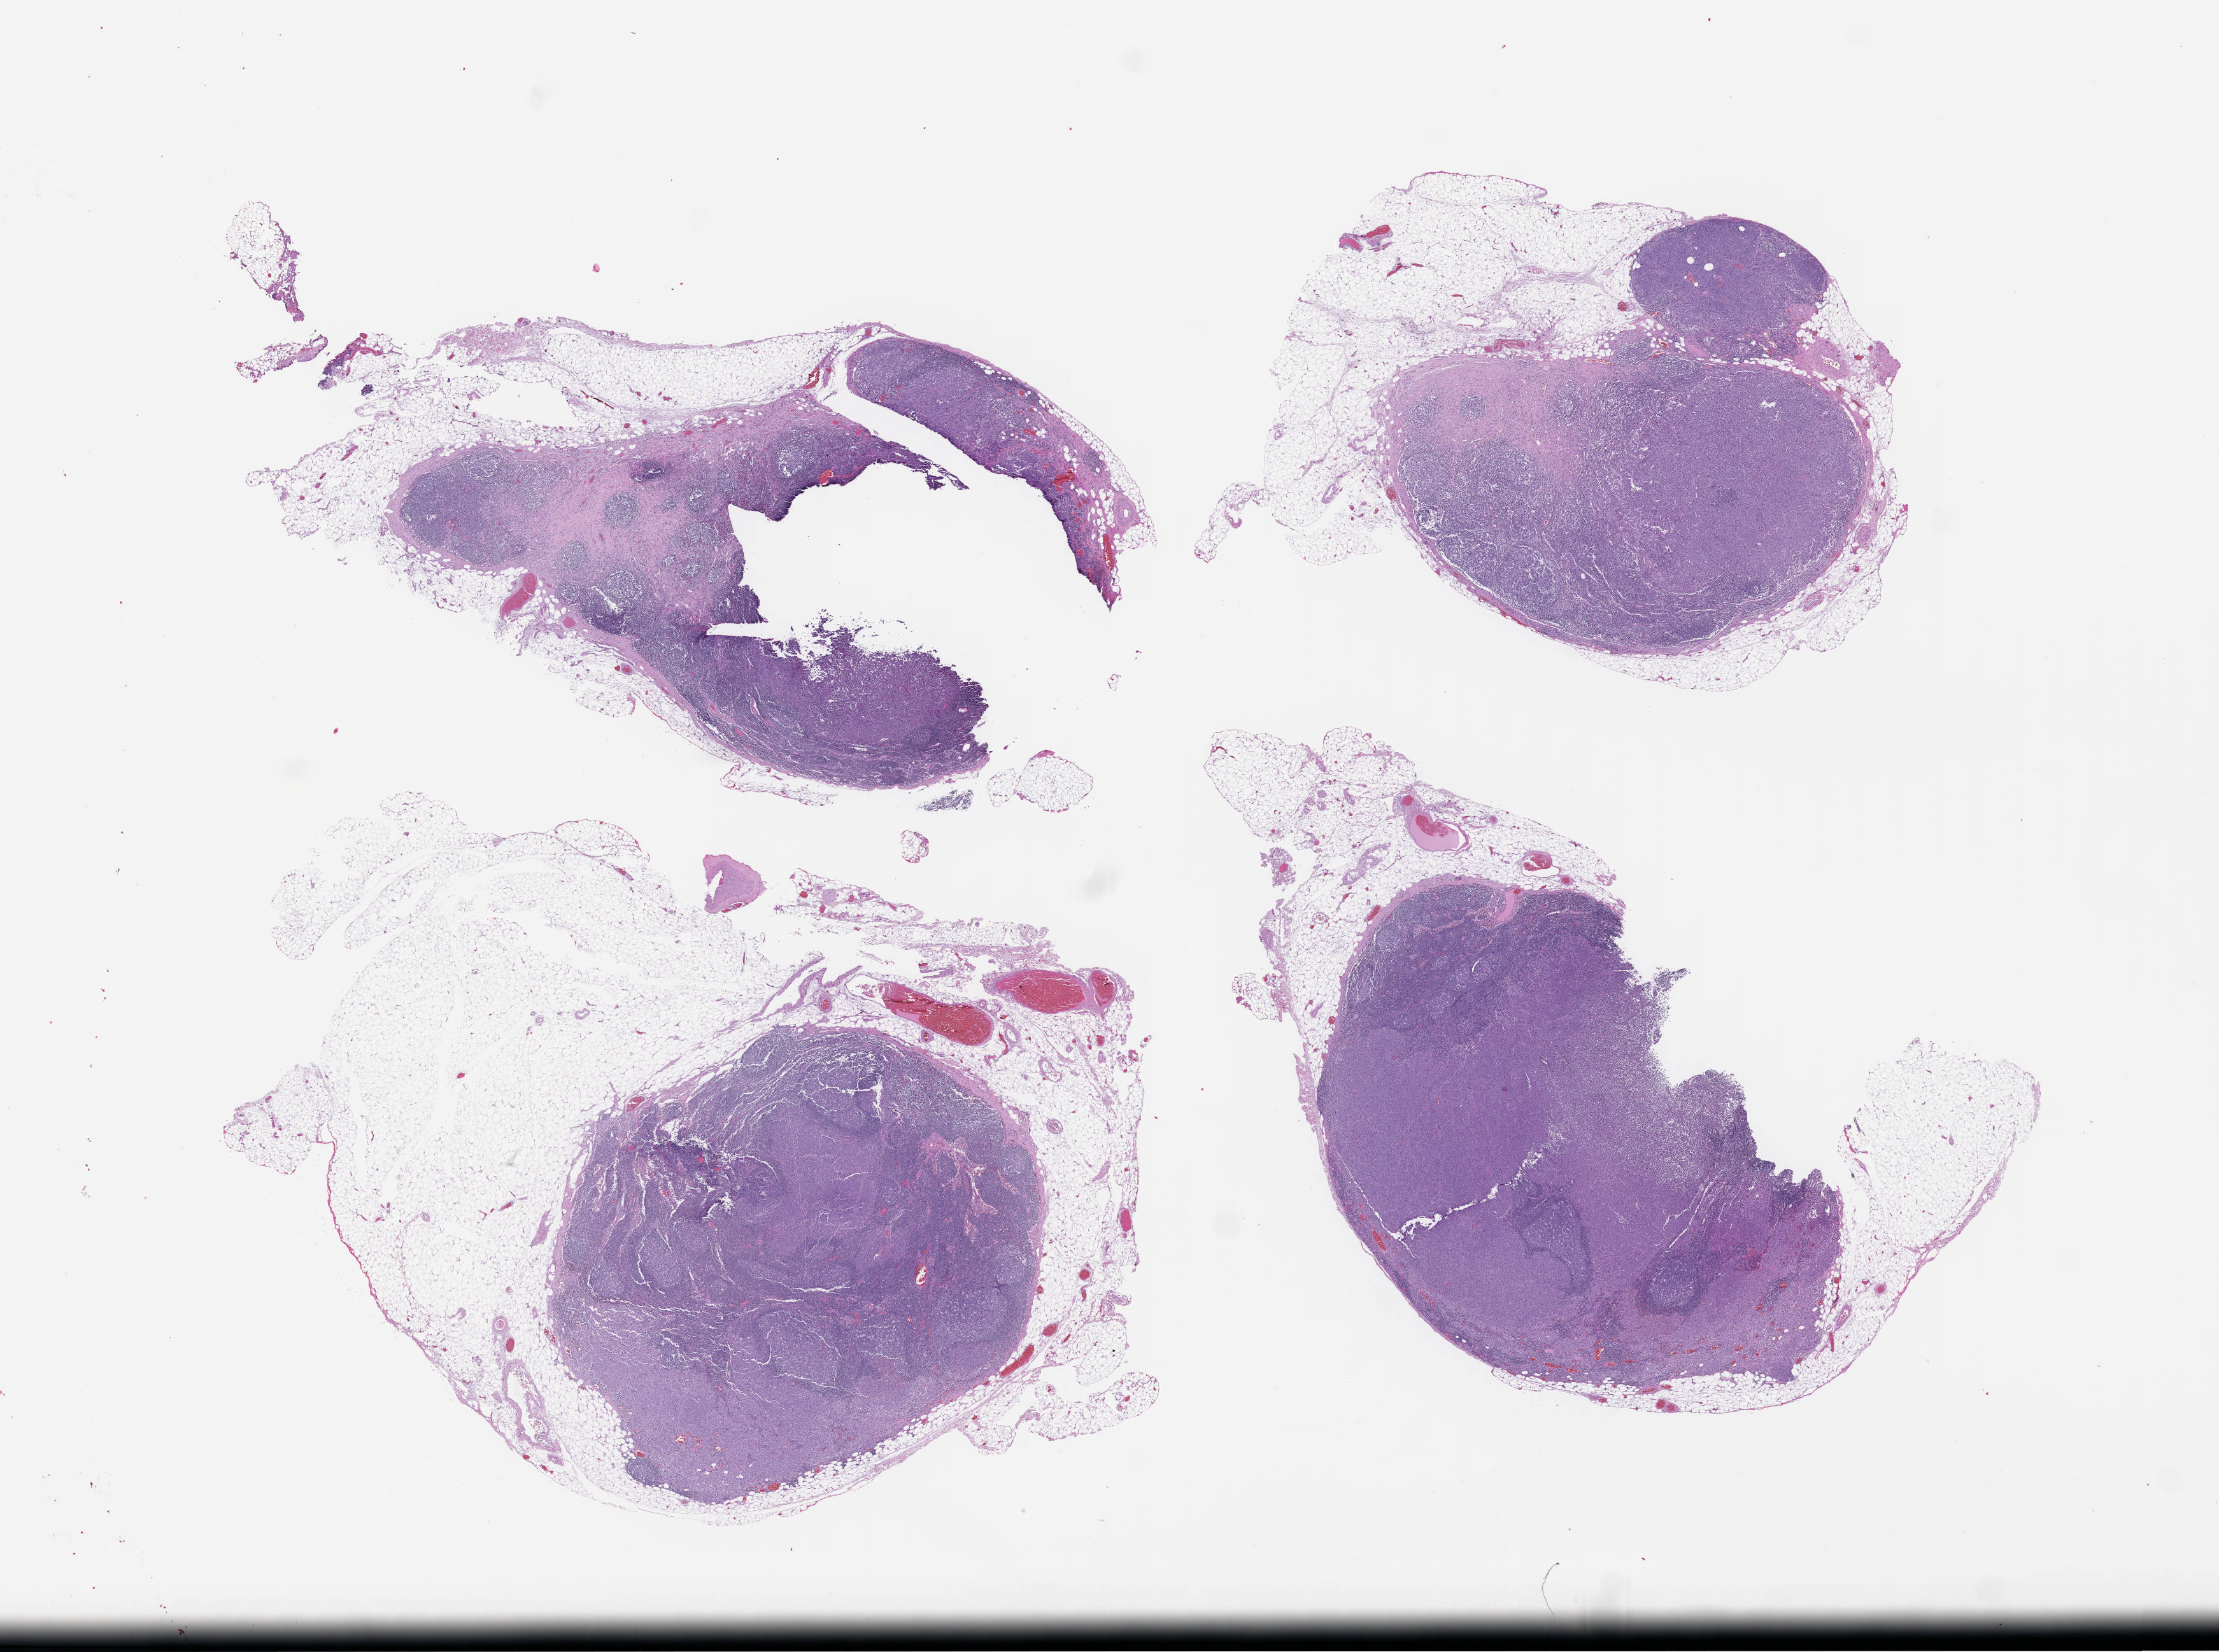
Digitized haematoxylin and eosin-stained section, whole scanned area (about 28.1 x 21.0 mm) shown as a low-resolution overview, formalin-fixed, paraffin-embedded (FFPE) tissue, specimen time point: archival tissue. Patient sex: male.
- this section: metastasis (sampled organ not recorded)
- primary diagnosis of the patient: Melanoma